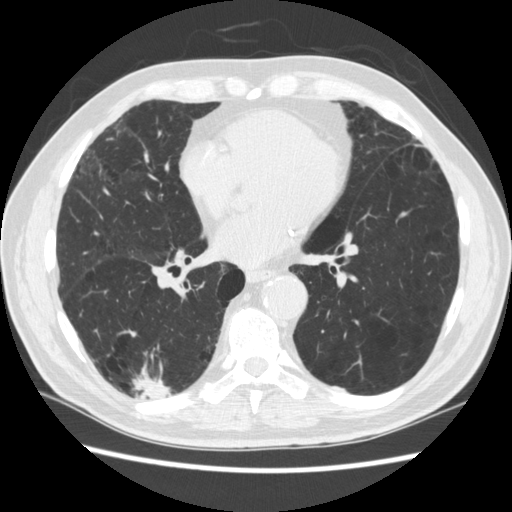
Low-dose screening chest CT, one axial slice; slice 118 of 266 in the series (ordered by position); reconstruction kernel STANDARD; 120 kVp; lung window (W 1500 / L -600 HU); 512 × 512 image matrix.
Annotated regions visible in this slice (outlined manually by an expert reader):
- lesion 1 (tumor, upper lobe of right lung): bounding box <134,373,170,399> (left, top, right, bottom; pixels)